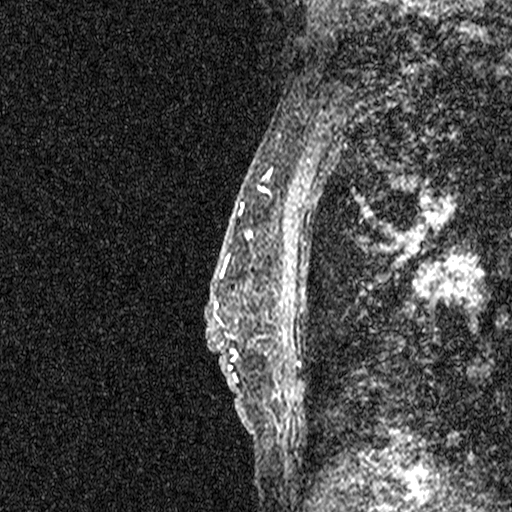
Breast MRI (dynamic contrast-enhanced), one sagittal slice; slice 19 of 44 in the series (ordered by position); dynamic contrast-enhanced study with each time point stored as its own series, time point 2 of 3 at this slice position (early post-contrast, ordered by acquisition time); 1.5 T; TE 4.5 ms, TR 11 ms; 2.05 mm slice thickness; 512 × 512 image matrix, field of view 200 × 200 mm. Female patient, age 44 years. Case-level facts recorded for this patient, not image findings: setting: breast cancer imaged before/during neoadjuvant chemotherapy; receptor status: HR-positive, HER2-negative.
Outlined on this slice (semi-automatic segmentation, software-assisted and operator-edited):
- analysis volume of interest (the breast-tissue region the enhancement analysis was run in; not a lesion): box from (x=204, y=254) to (x=317, y=401) px
- tumour enhancement mask (voxels above the 90 % enhancement threshold inside the analysis volume of interest): (x=206, y=254)–(x=304, y=394)